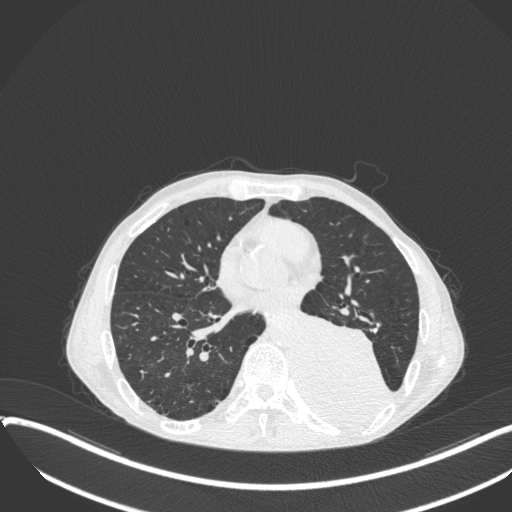
Chest CT, one axial slice; slice 157 of 400 in the series (ordered by position); reconstruction kernel B31f; lung window (W 1500 / L -600 HU); 512 × 512 image matrix, field of view 400 × 400 mm. Patient: male, 57 years. From the clinical record (not read from this slice): clinical TNM (as recorded): T4 N0 M0.
Outlined on this slice (bounding box drawn by a radiologist):
- lung tumour (recorded histology: squamous cell carcinoma): bounding box [x1, y1, x2, y2] px = [294, 307, 395, 437]